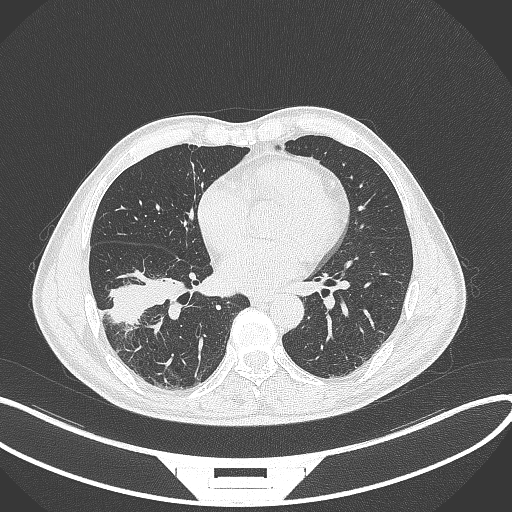
Chest CT, one axial slice; slice 153 of 364 in the series (ordered by position); 120 kVp; lung window (W 1500 / L -600 HU); 512 × 512 image matrix, field of view 400 × 400 mm. Male patient, age 58 years. Case-level facts recorded for this patient, not image findings: clinical TNM (as recorded): T3 N0 M0; histopathological grade: G2.
Structures marked on this image (bounding box drawn by a radiologist):
- lung tumour (recorded histology: squamous cell carcinoma): bounding box <108,274,194,332> (left, top, right, bottom; pixels)